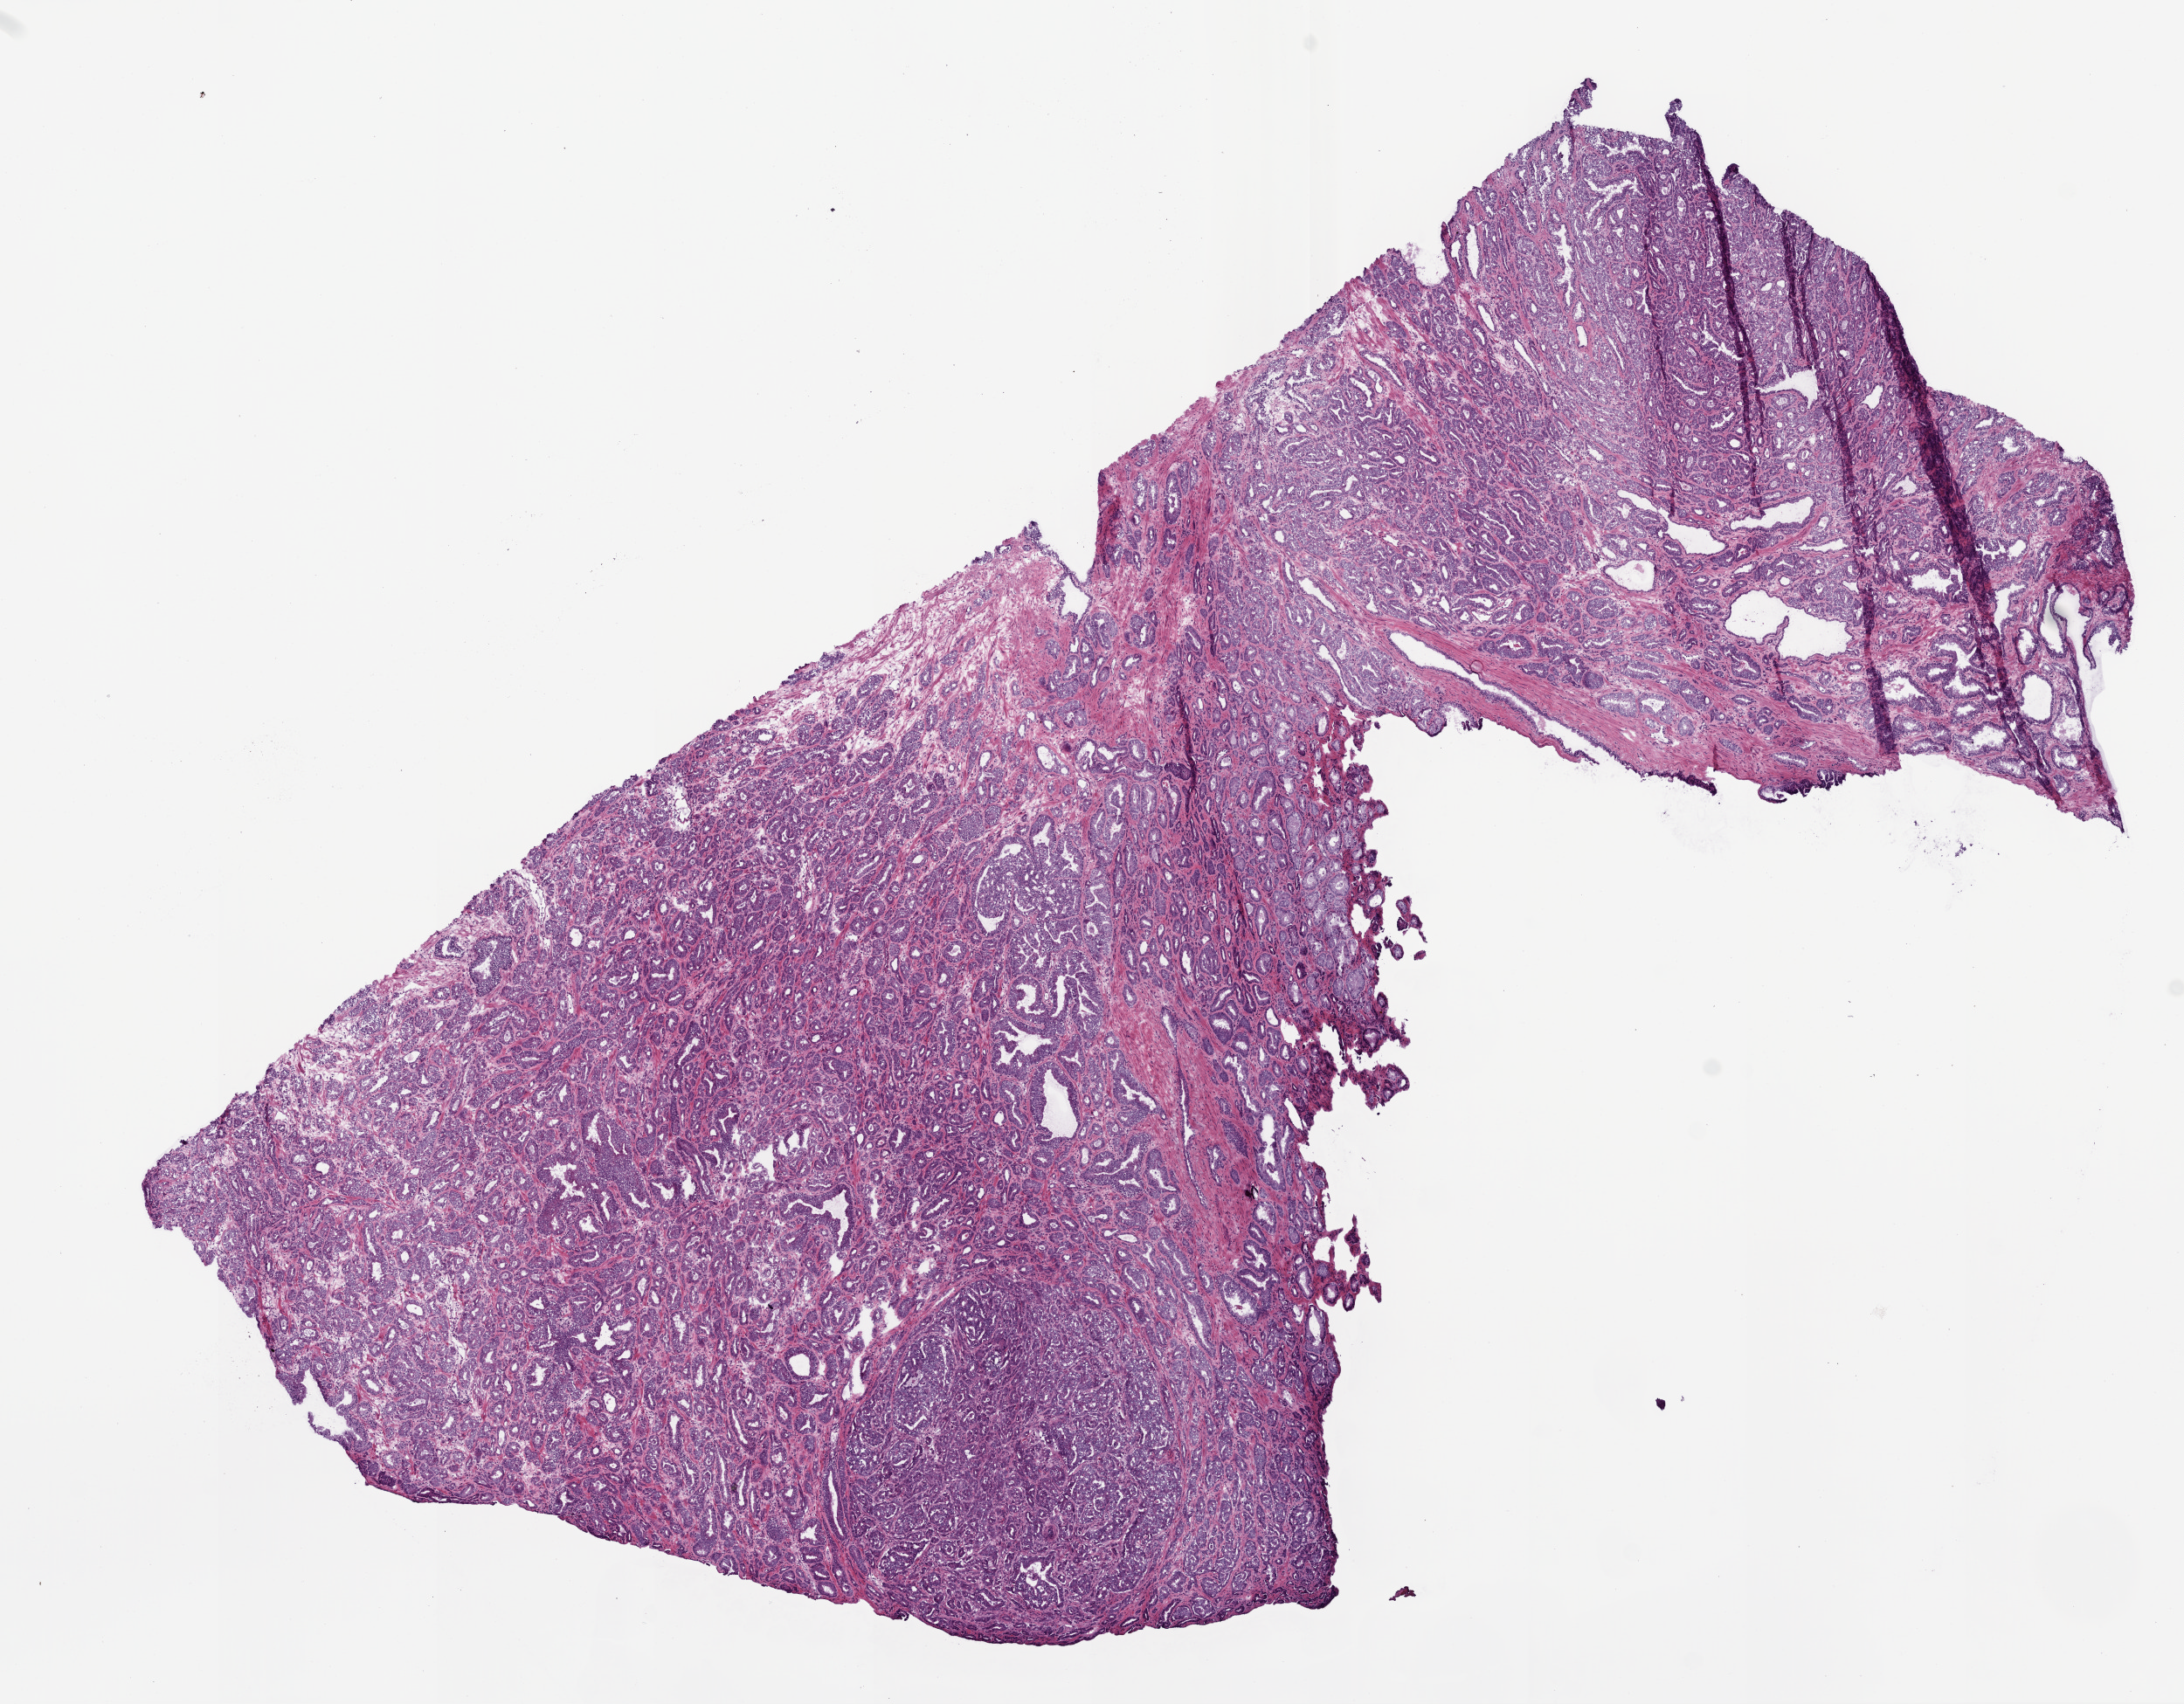
Whole-slide histology image, Hematoxylin and eosin (H&E) stained, low-resolution overview of the scanned area, about 10.0 x 7.8 mm (from a 20x scan). Frozen section from the top of the tissue portion. Sample: primary tumour, prostate. Male patient; age at initial diagnosis 57 years.
Histologic diagnosis: Acinar cell carcinoma (prostate gland).